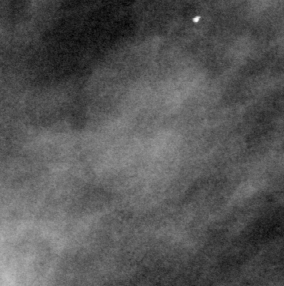
Region of interest cut from a scanned film mammogram (one marked finding), right breast, MLO view.
Mass, shape oval, margins circumscribed; BI-RADS assessment category 3; pathology result (as recorded, not read from the image): benign.